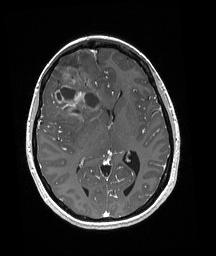
Brain MRI from a brain-tumour surgery series, one axial slice; slice 97 of 192 in the series (ordered by position); T1-weighted post-contrast; 216 × 256 image matrix, field of view 211 × 250 mm. Case-level facts recorded for this patient, not image findings: histopathology: Oligodendroglioma; WHO grade: 3; IDH mutation: yes; tumour location: Right Frontal.
Structures marked on this image (manually delineated by an expert):
- tumour: bounding box (x1, y1, x2, y2) in pixels: (48, 58, 100, 117)